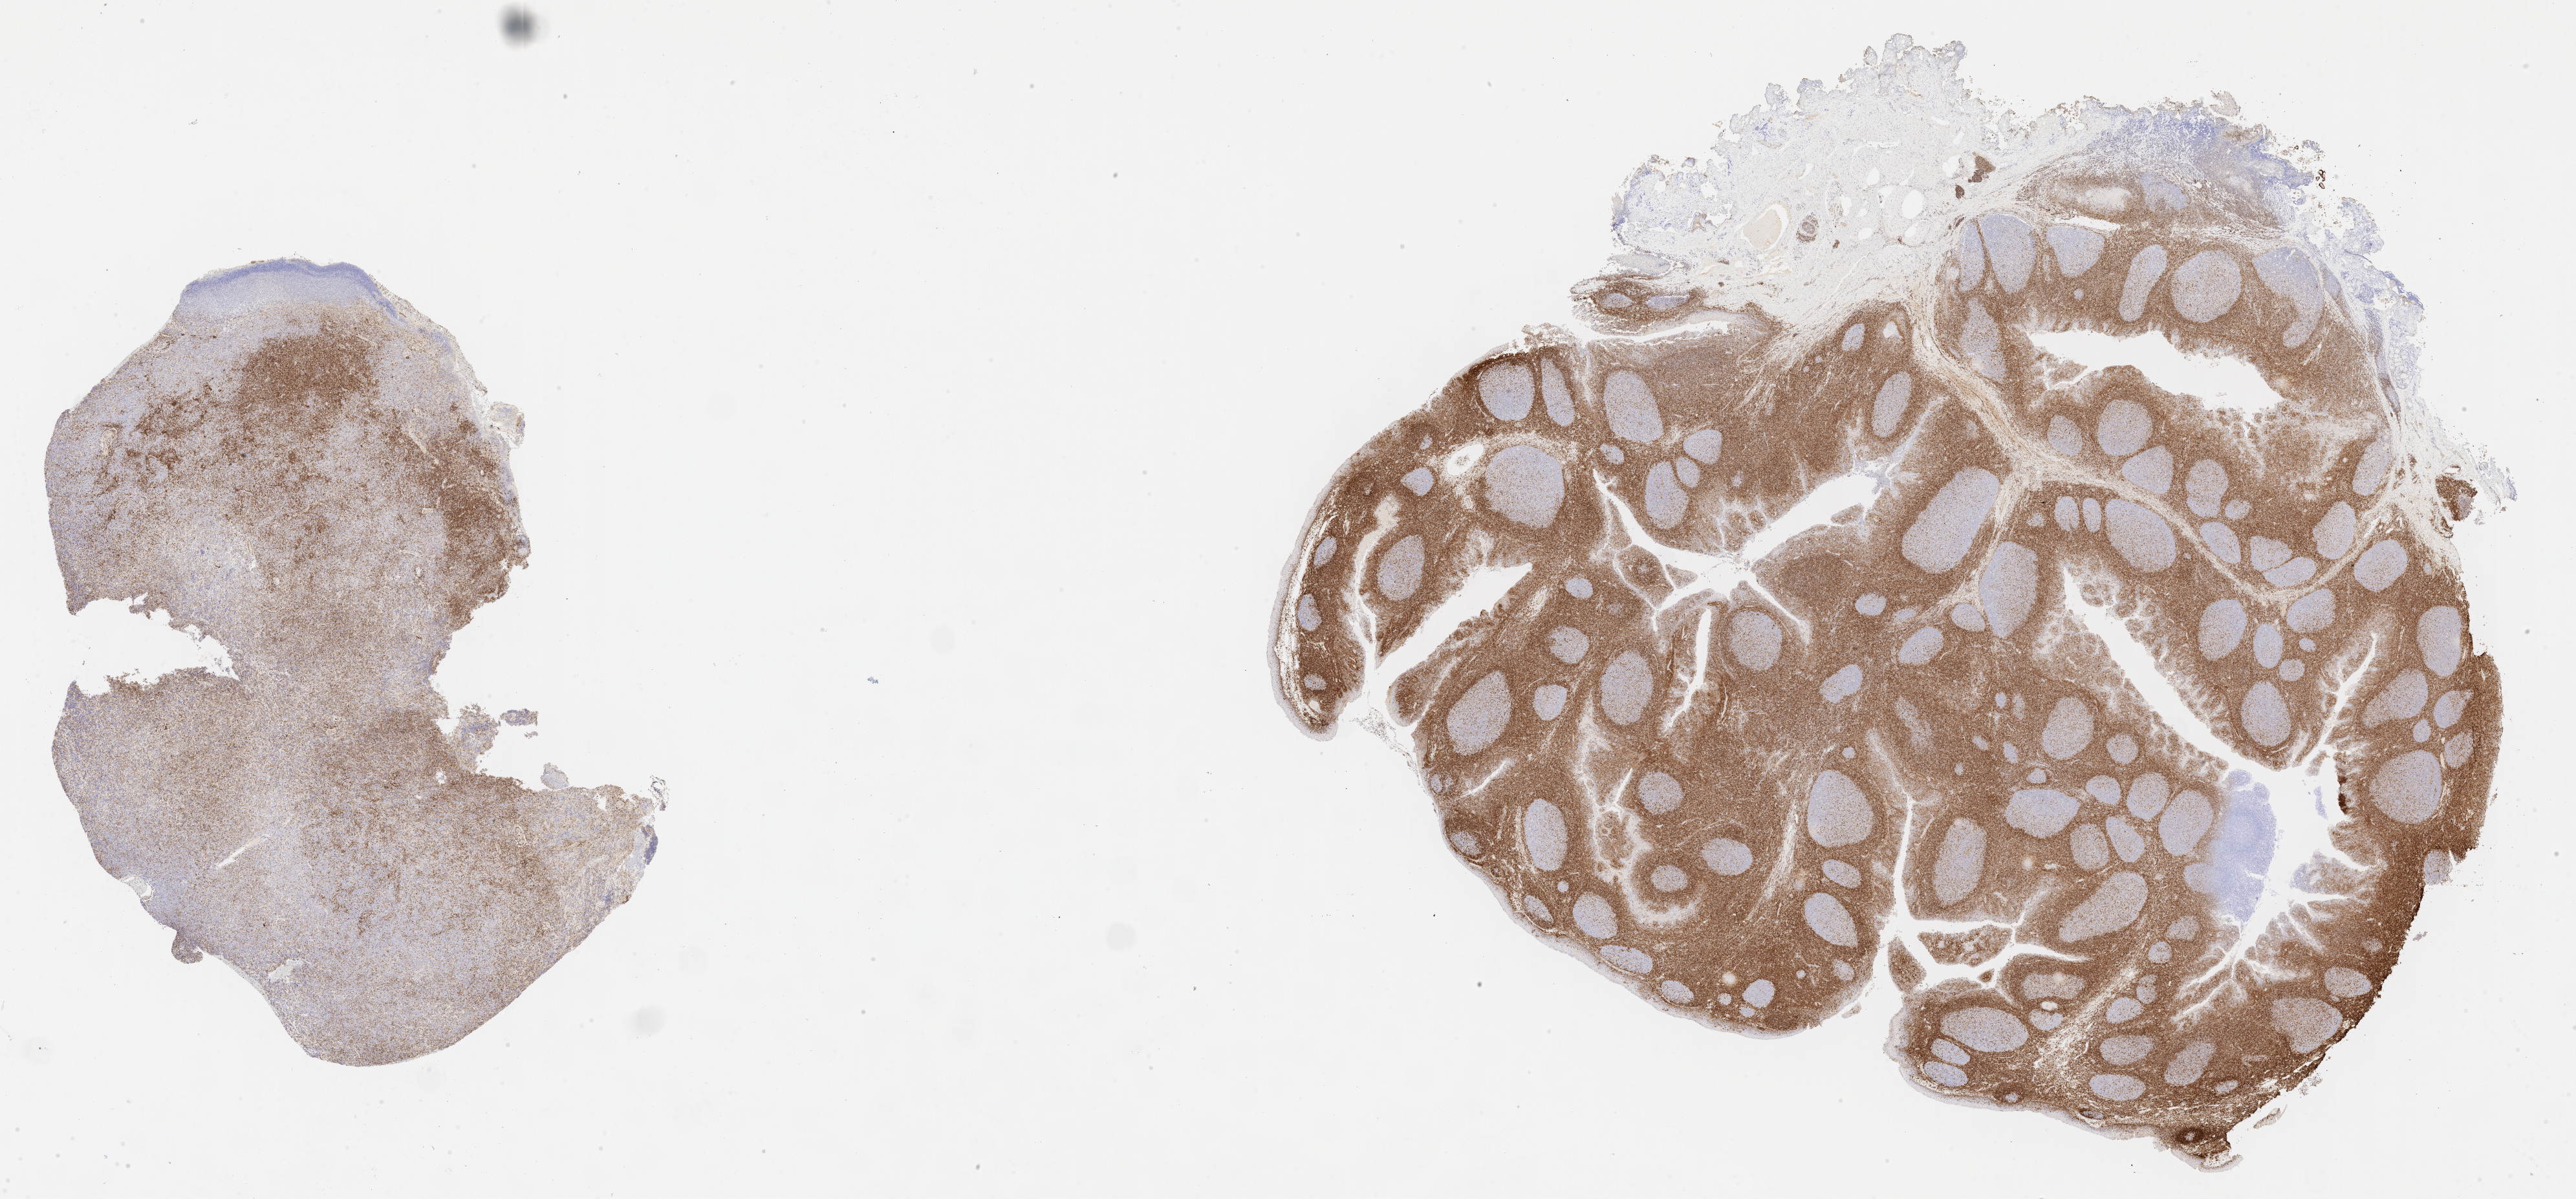
IHC for BCL2, whole-slide image — a low-resolution overview of the entire scanned area, about 32.2 x 15.0 mm; specimen: tumor tissue. Male patient; age at initial diagnosis 7 years.
• histologic diagnosis: Diffuse large B-cell lymphoma, NOS